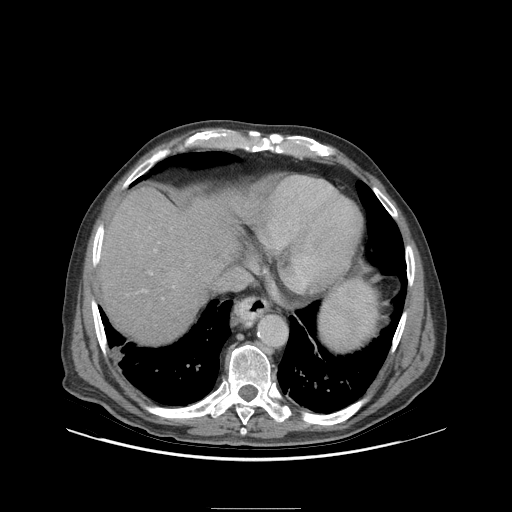
Contrast-enhanced abdominal CT (liver protocol), one axial slice; slice 85 of 105 in the series (ordered by position); 140 kVp; soft-tissue window (W 400 / L 40 HU); 512 × 512 image matrix, field of view 440 × 440 mm. From the clinical record (not read from this slice): diagnosis: hepatocellular carcinoma (patient treated with transarterial chemoembolisation; whether this scan precedes or follows treatment is not stated here); TNM stage (as recorded): Stage-I; Child-Pugh class: A; tumour nodularity: uninodular; tumour size: 5.1 cm.
Annotated regions visible in this slice (semi-automatically segmented with operator editing):
- abdominal aorta: box from (x=260, y=316) to (x=286, y=344) px
- liver parenchyma outside the tumour (the mass and vessels are separate outlines, so this box may not span the whole liver): (x=98, y=186)–(x=244, y=342)
- liver vessels: (x=151, y=250)–(x=156, y=274)